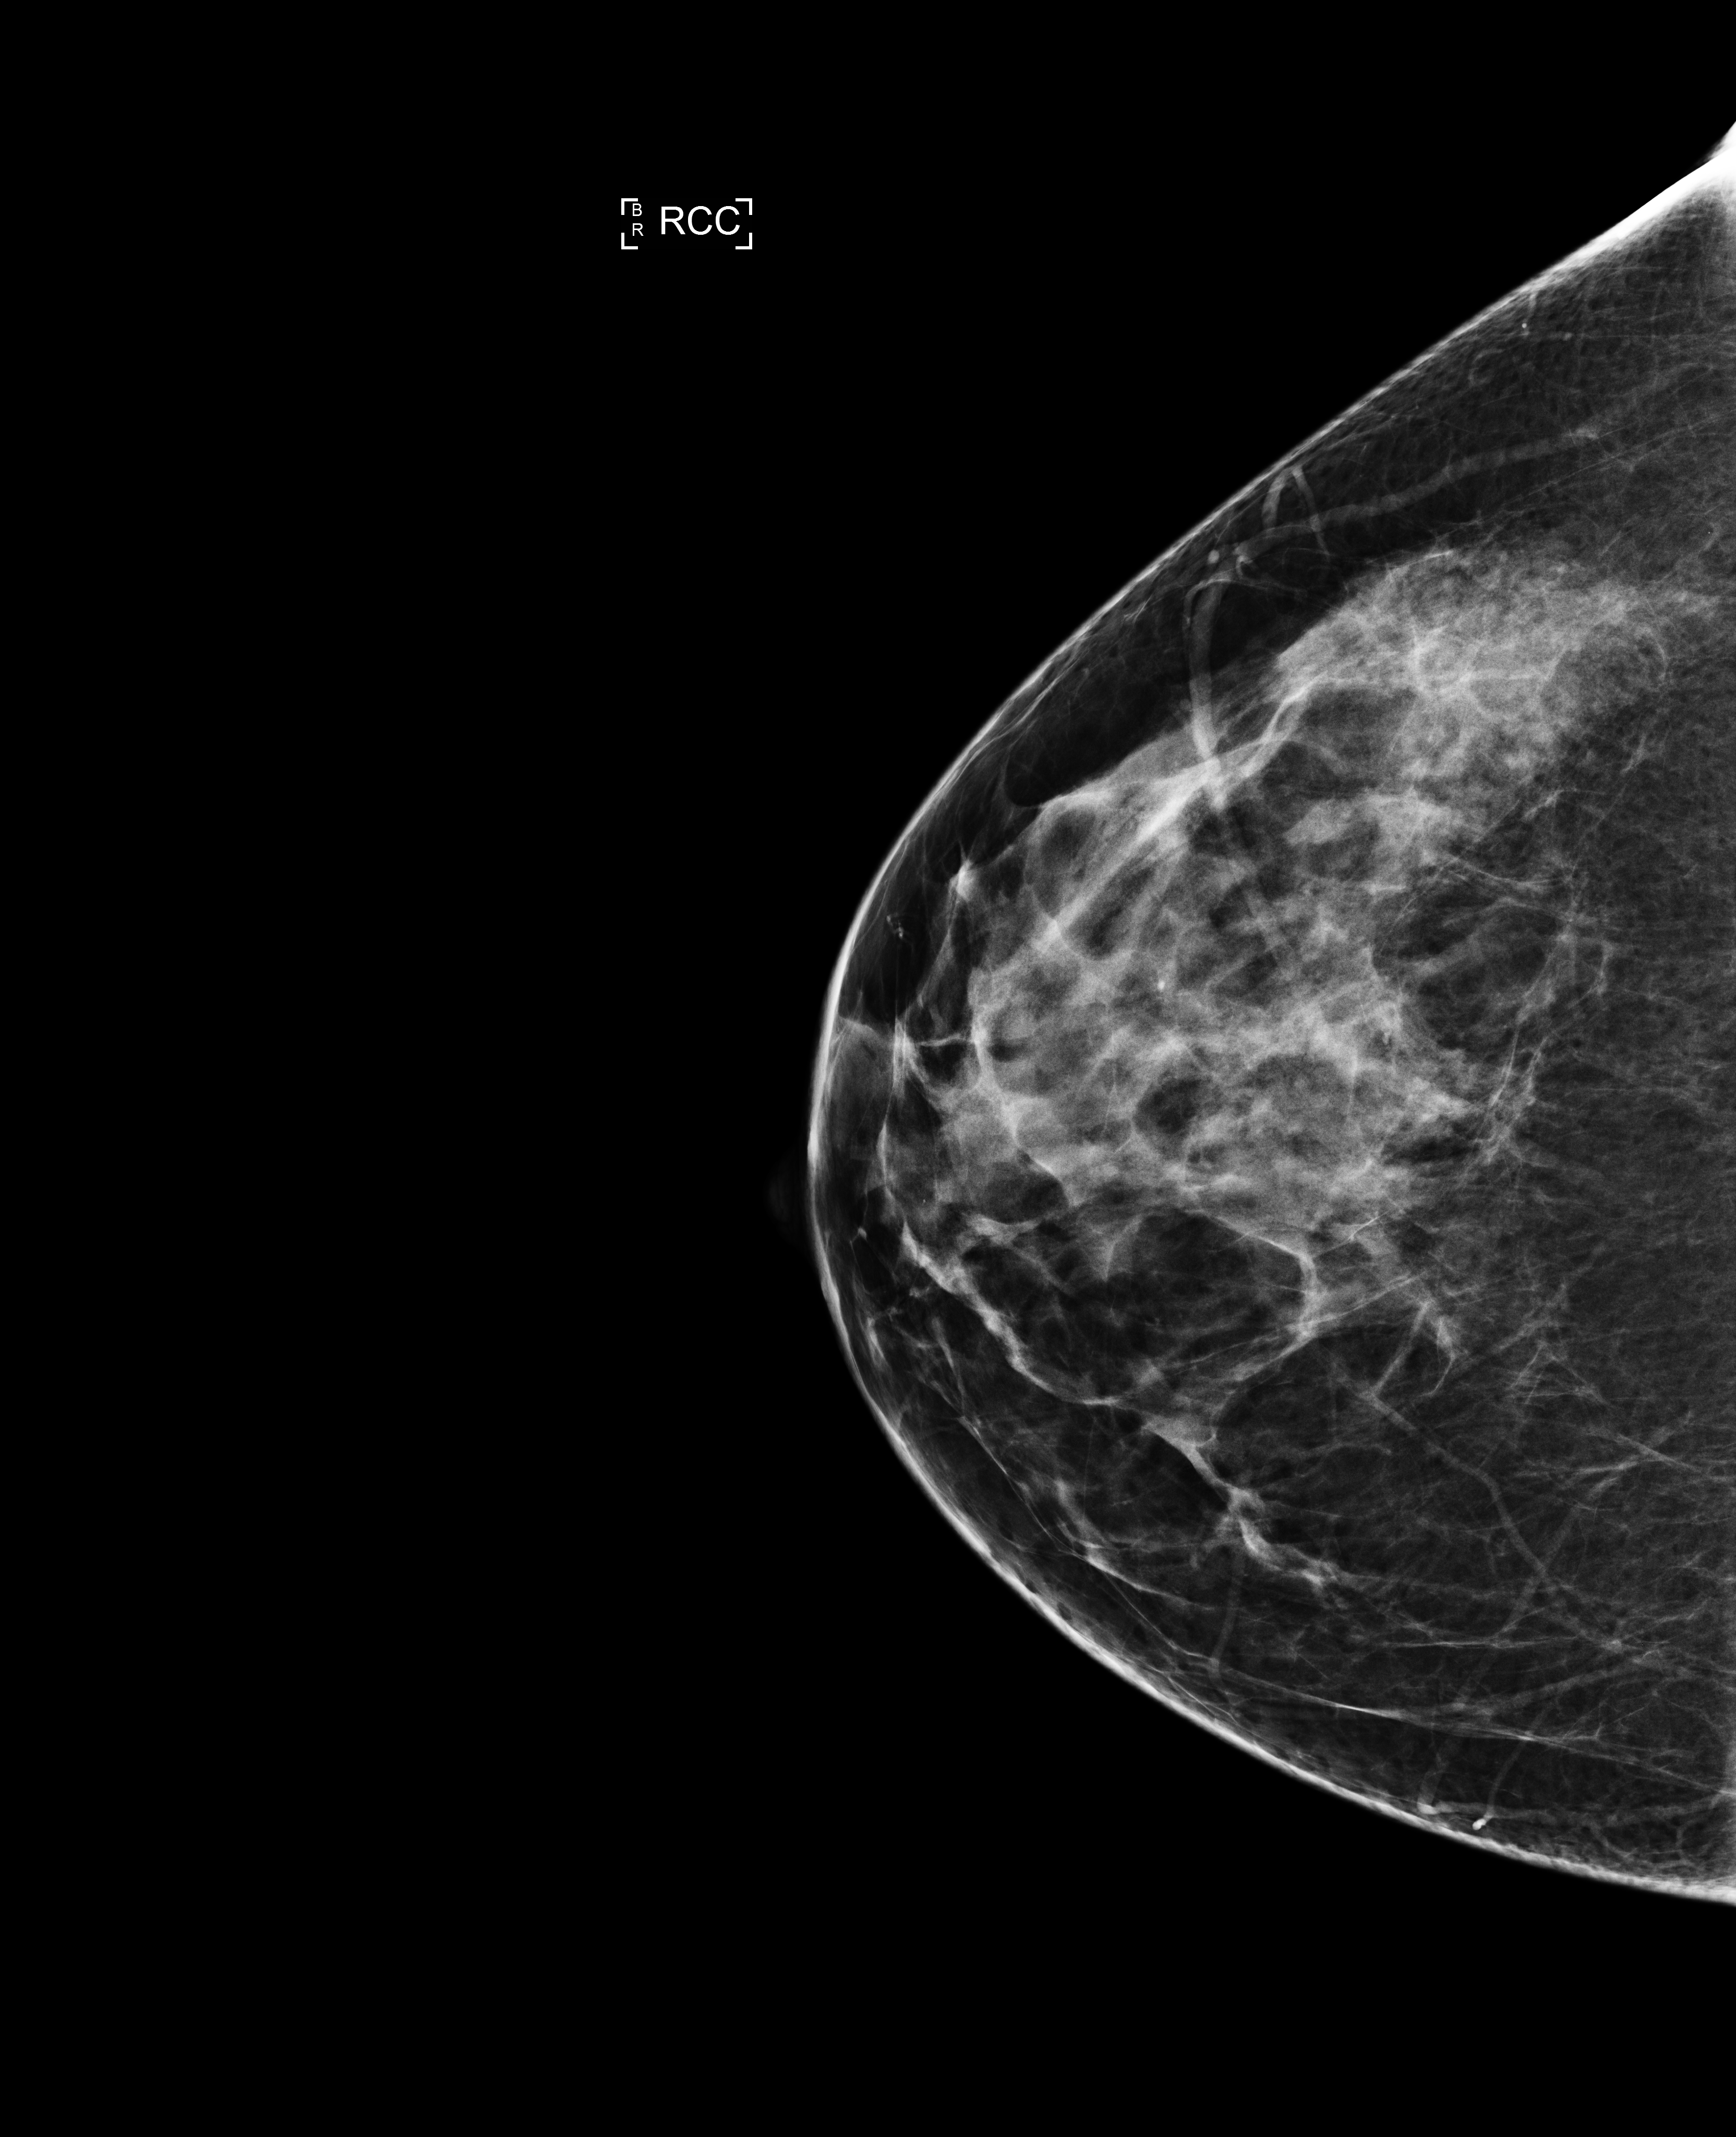
Annual screening mammography examination, compressed breast thickness 66 mm. Patient aged 46 years (female).
Image type: full-field digital mammogram. Breast: right. Projection: CC view.